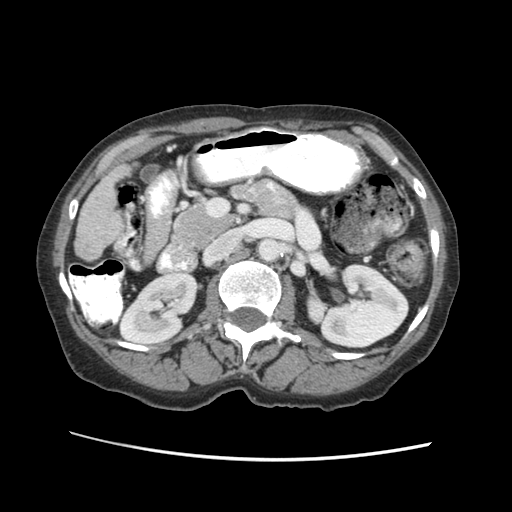
Contrast-enhanced abdominal CT (liver protocol), one axial slice; position 12 of 63 along the scan axis; soft-tissue window (W 400 / L 40 HU); 2.5 mm slice thickness; 512 × 512 image matrix. Case-level facts recorded for this patient, not image findings: diagnosis: hepatocellular carcinoma (patient treated with transarterial chemoembolisation; whether this scan precedes or follows treatment is not stated here); TNM stage (as recorded): Stage-I; Child-Pugh class: B; tumour differentiation: well differentiated; tumour nodularity: uninodular.
Structures marked on this image (semi-automatically segmented with operator editing):
- liver parenchyma outside the tumour (the mass and vessels are separate outlines, so this box may not span the whole liver): bounding box [x1, y1, x2, y2] px = [74, 166, 124, 260]